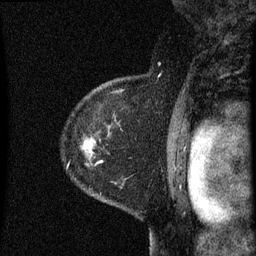
Breast MRI (dynamic contrast-enhanced), one sagittal slice. Position 46 of 60 along the scan axis. Dynamic contrast-enhanced series, image 2 of 3 at this slice position (ordered by acquisition). 1.5 T. TE 4.2 ms, TR 8 ms. 2 mm slice thickness. 256 × 256 image matrix, field of view 180 × 180 mm. Female patient, age 60 years.
Annotated regions visible in this slice (semi-automatic segmentation, software-assisted and operator-edited):
- analysis volume of interest (the breast-tissue region the enhancement analysis was run in; not a lesion): box from (x=82, y=82) to (x=118, y=167) px
- tumour enhancement mask (voxels above the 70 % enhancement threshold inside the analysis volume of interest): (x=87, y=144)–(x=91, y=147)